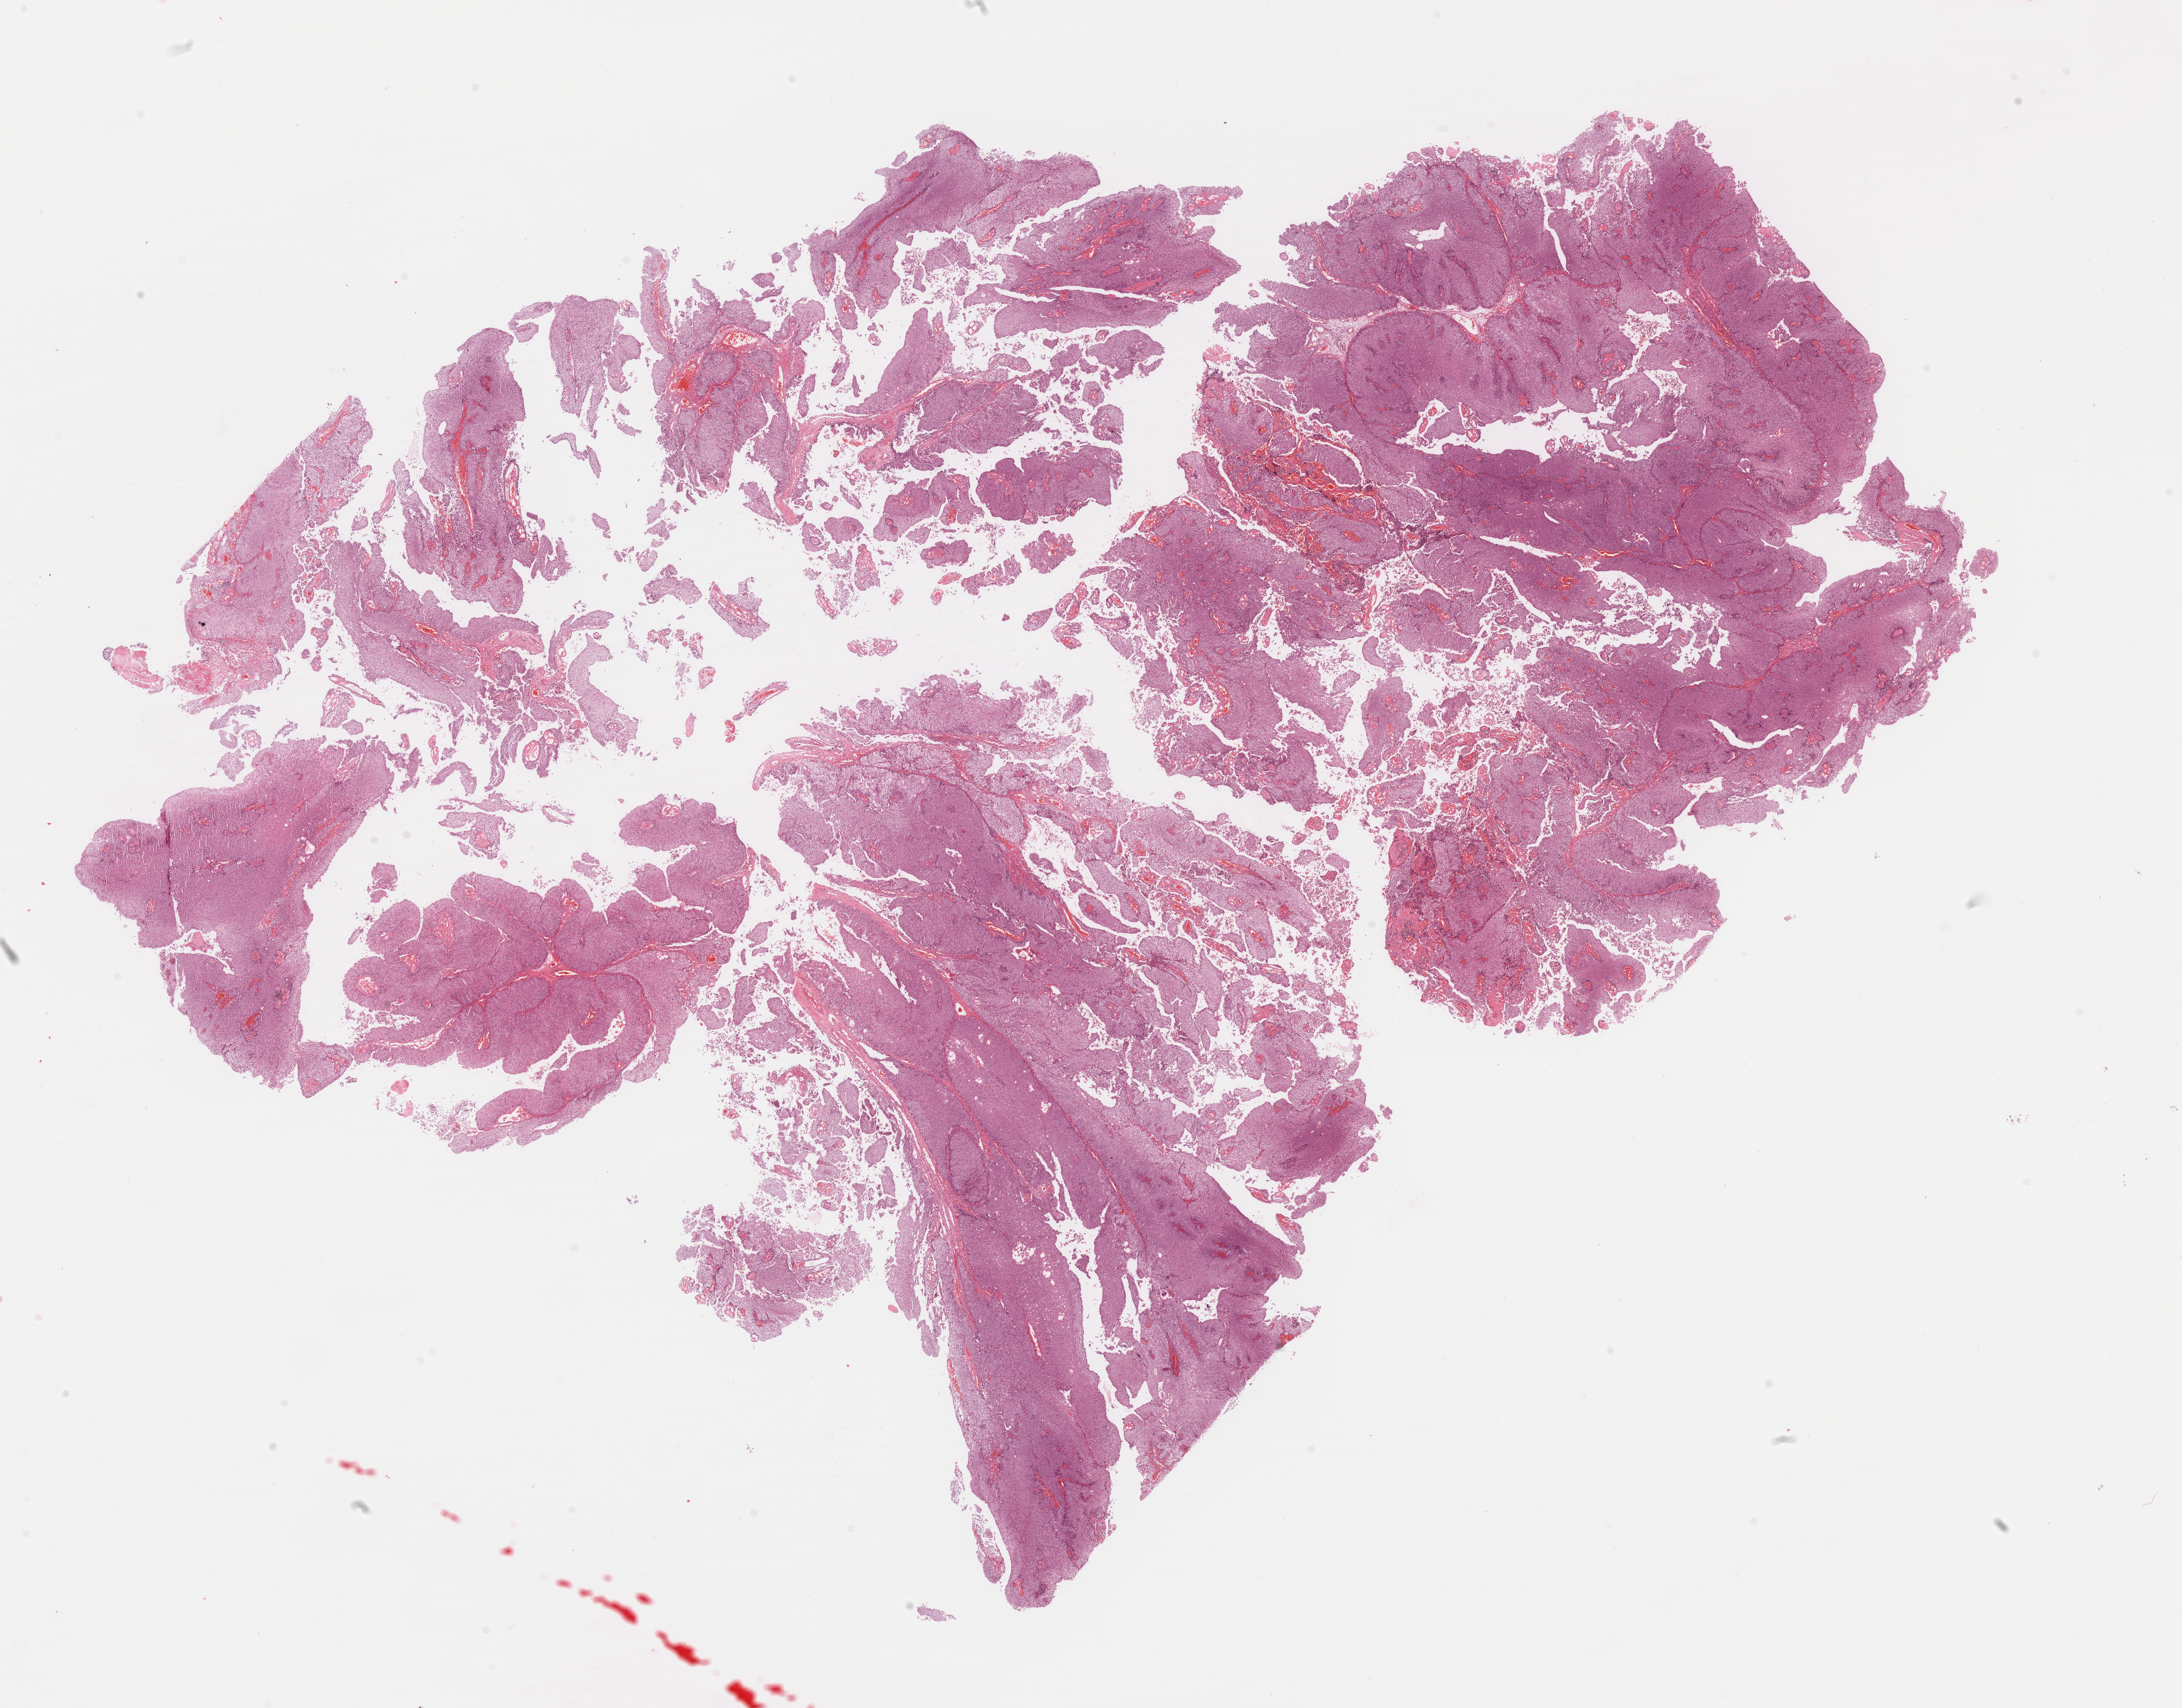
Whole-slide histology image, Hematoxylin and eosin (H&E) stained, low-resolution overview of the scanned area, about 24.2 x 18.9 mm (acquisition: 40x scan). Formalin-fixed paraffin-embedded (FFPE) diagnostic section. Sample: primary tumour, bladder. Male, age 57 years at initial diagnosis. Histologic grade: low grade.
AJCC pathologic stage: II (7th edition). Histologic diagnosis: Transitional cell carcinoma.